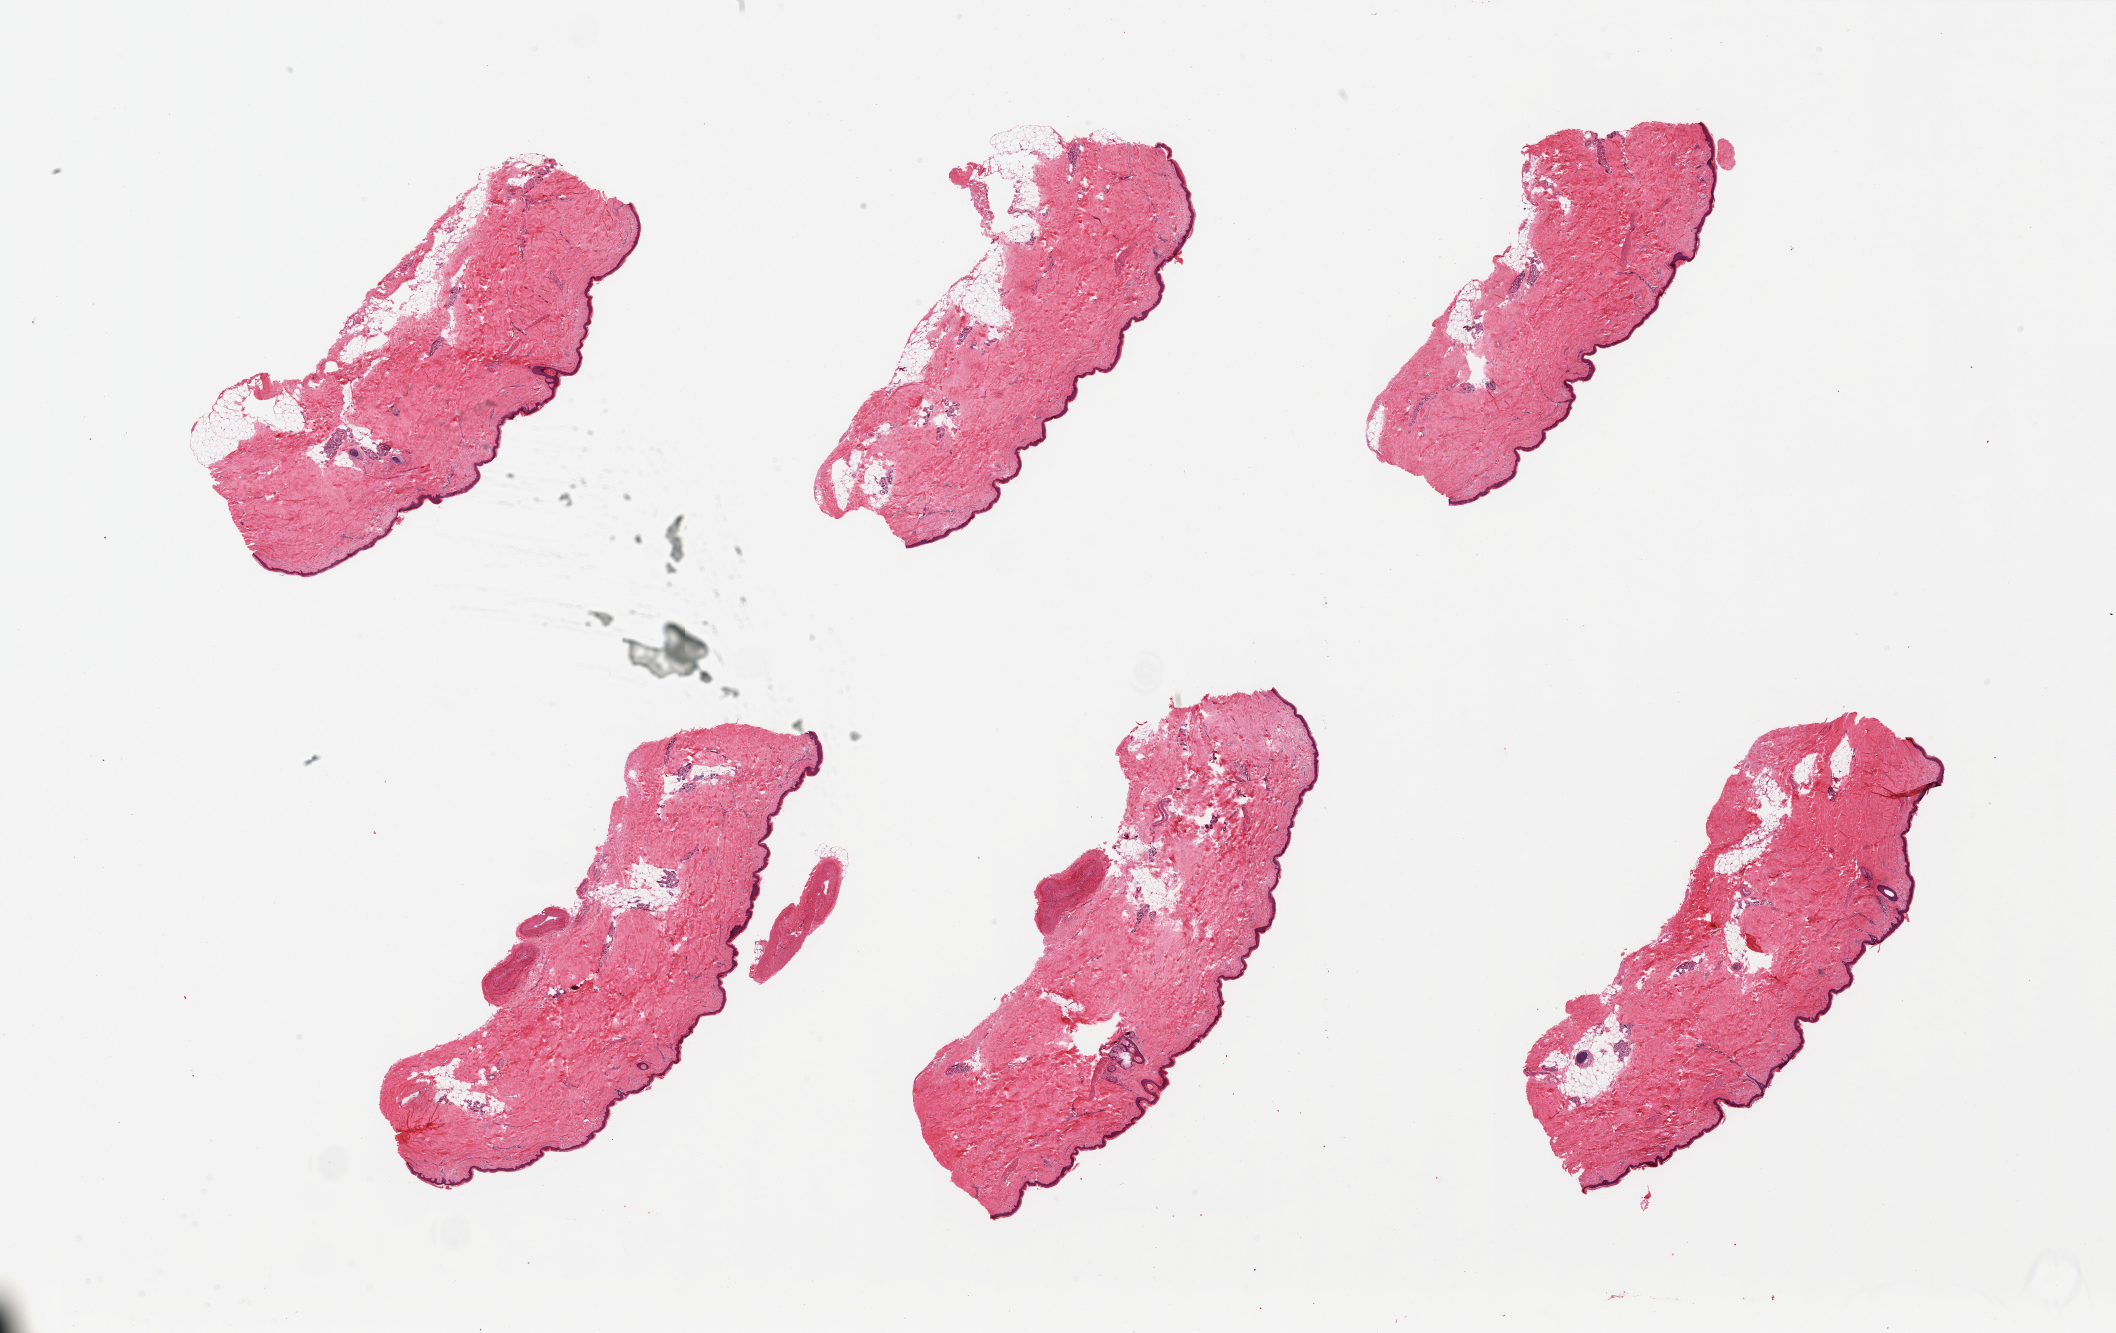
Digitized H&E-stained section — low-resolution overview of the scanned area, about 33.5 x 21.1 mm (from a 20x scan). PAXgene-fixed paraffin-embedded (PFPE) section. Target tissue: skin of lower leg. Tissue donor sample. Donor sex: male.
Reviewer comment on this tissue sample: 6 pieces, squamous epithelium is ~30-40 microns.